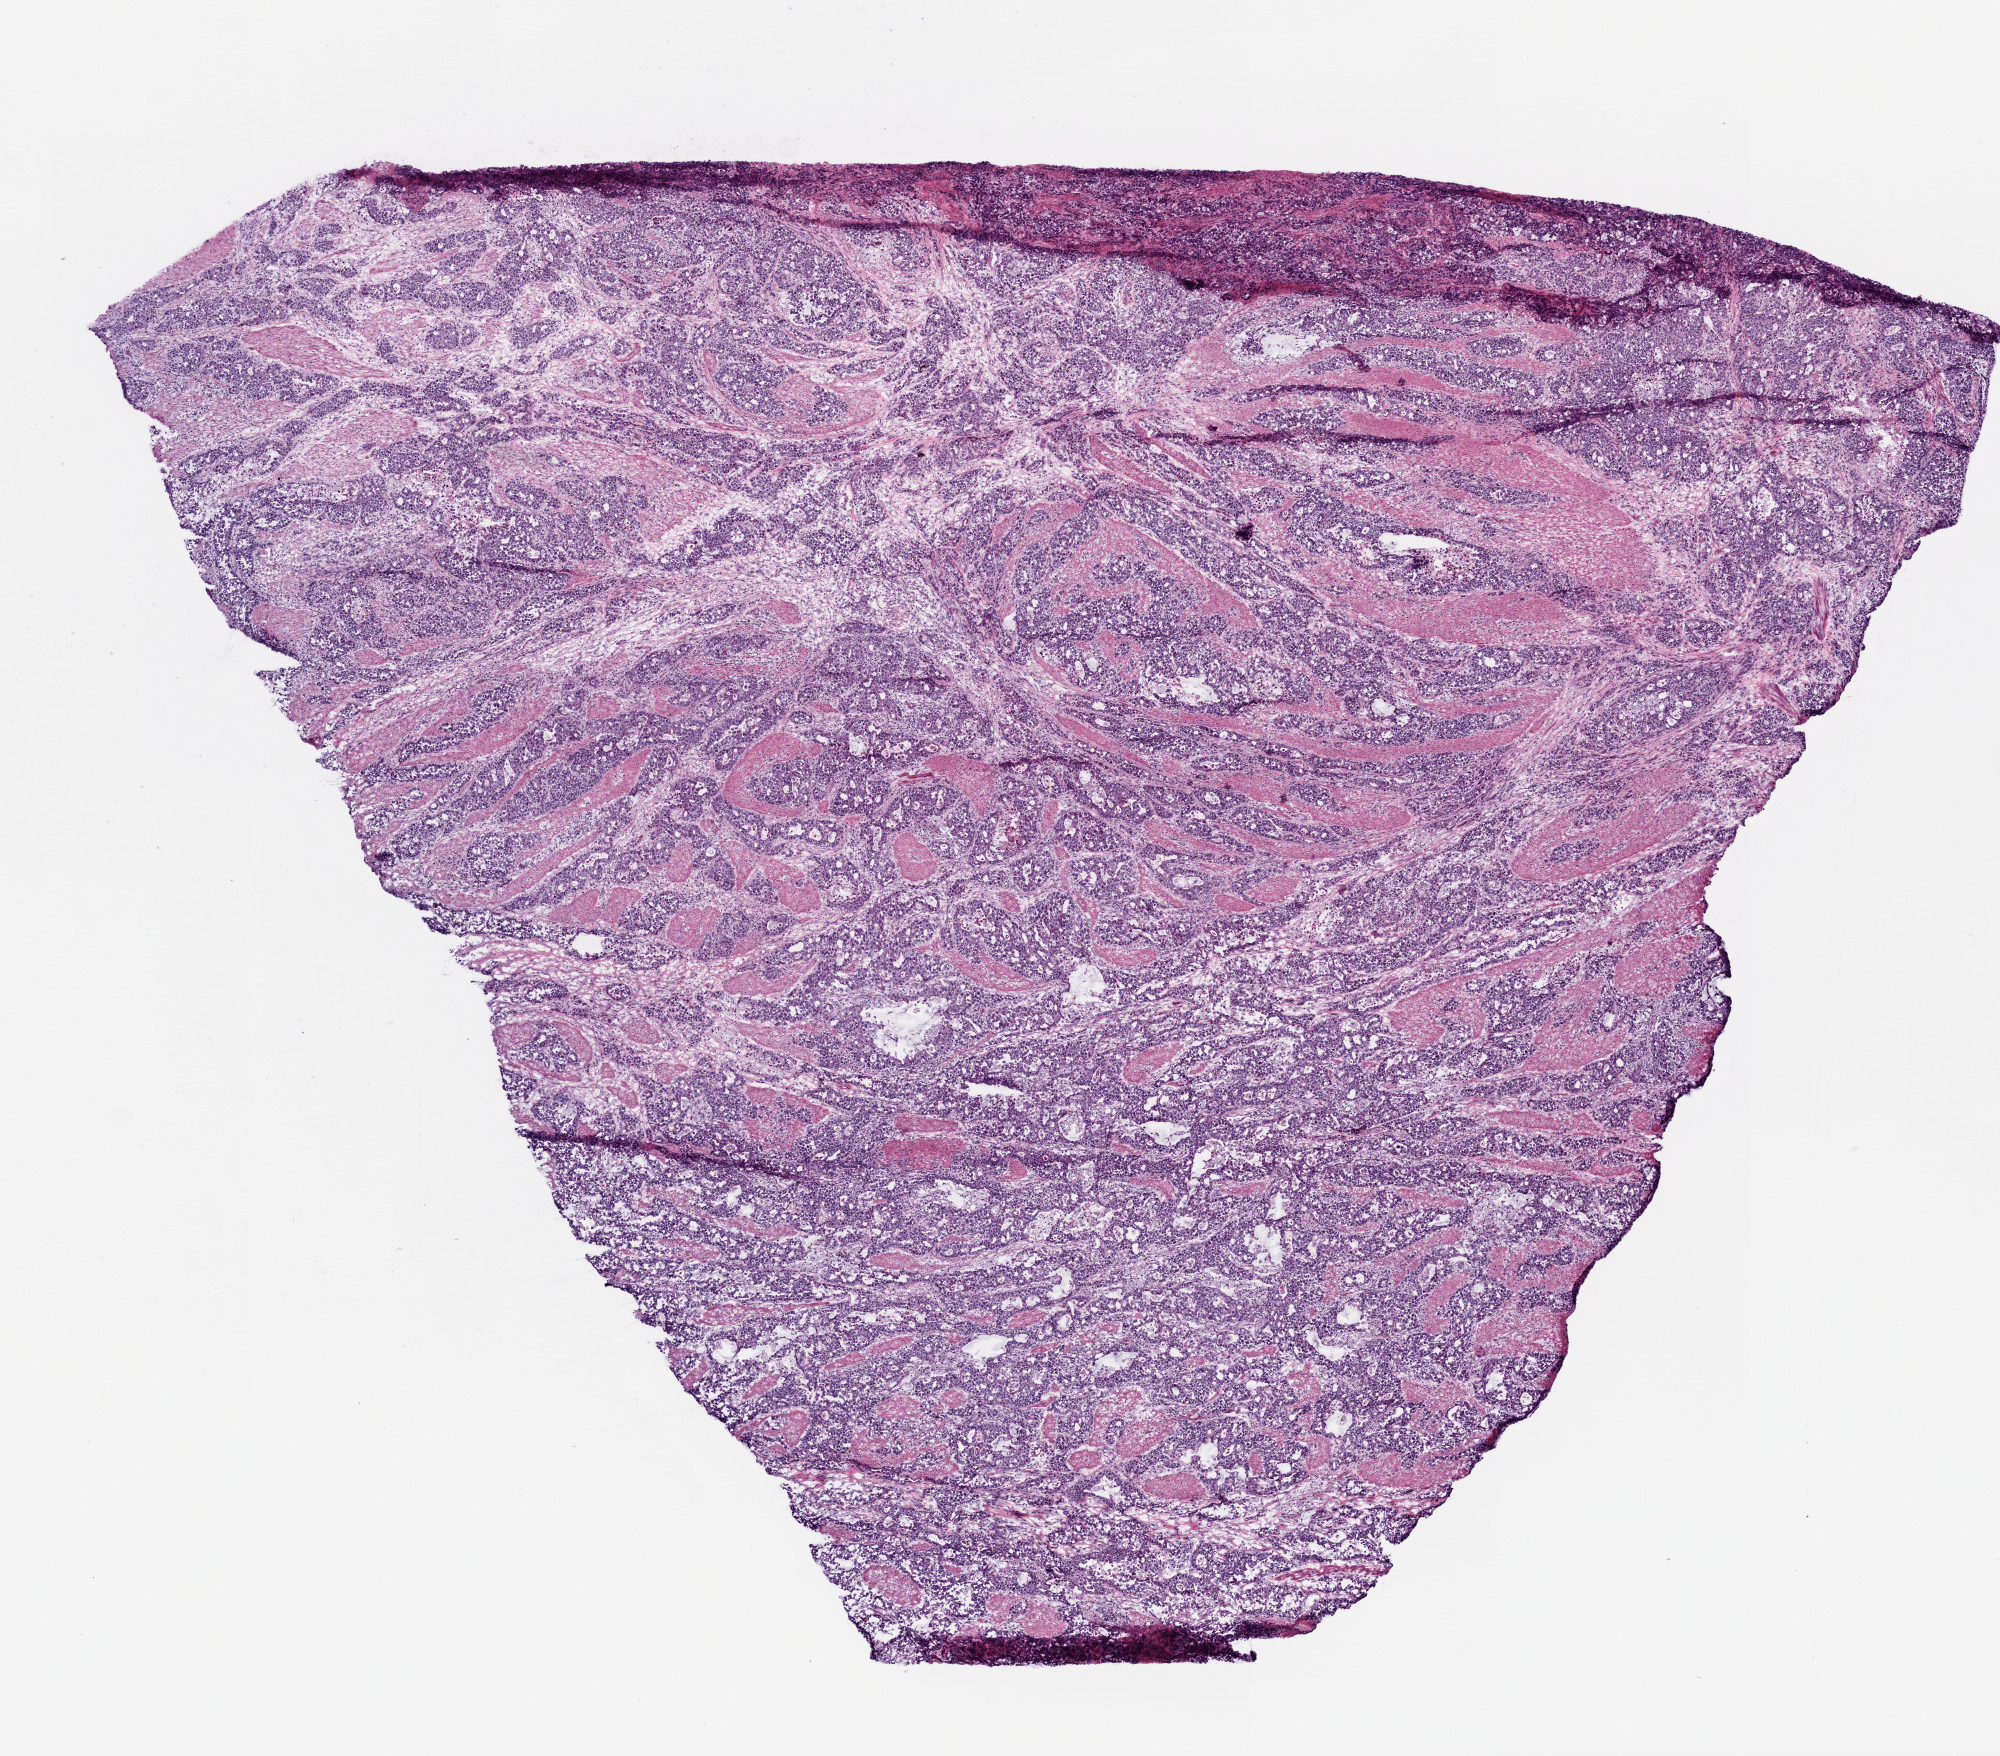
Whole-slide histology image, H&E-stained, a low-resolution overview of the entire scanned area, about 8.0 x 7.0 mm (from a 20x scan). Frozen section from the top of the tissue portion. Stomach, primary tumour sample. Patient: male, age at initial diagnosis 56 years. Histologic grade: G3 (poorly differentiated). Composition of this section per pathologist review: tumour cells 85%, tumour nuclei 80%, normal cells 0%, stromal cells 15%, necrosis 5%.
TNM: T4 N2 M0. AJCC pathologic stage: IV (5th edition). Histologic diagnosis: Adenocarcinoma, intestinal type (gastric antrum). Lymph nodes positive (case pathology): 14 of 35 examined.